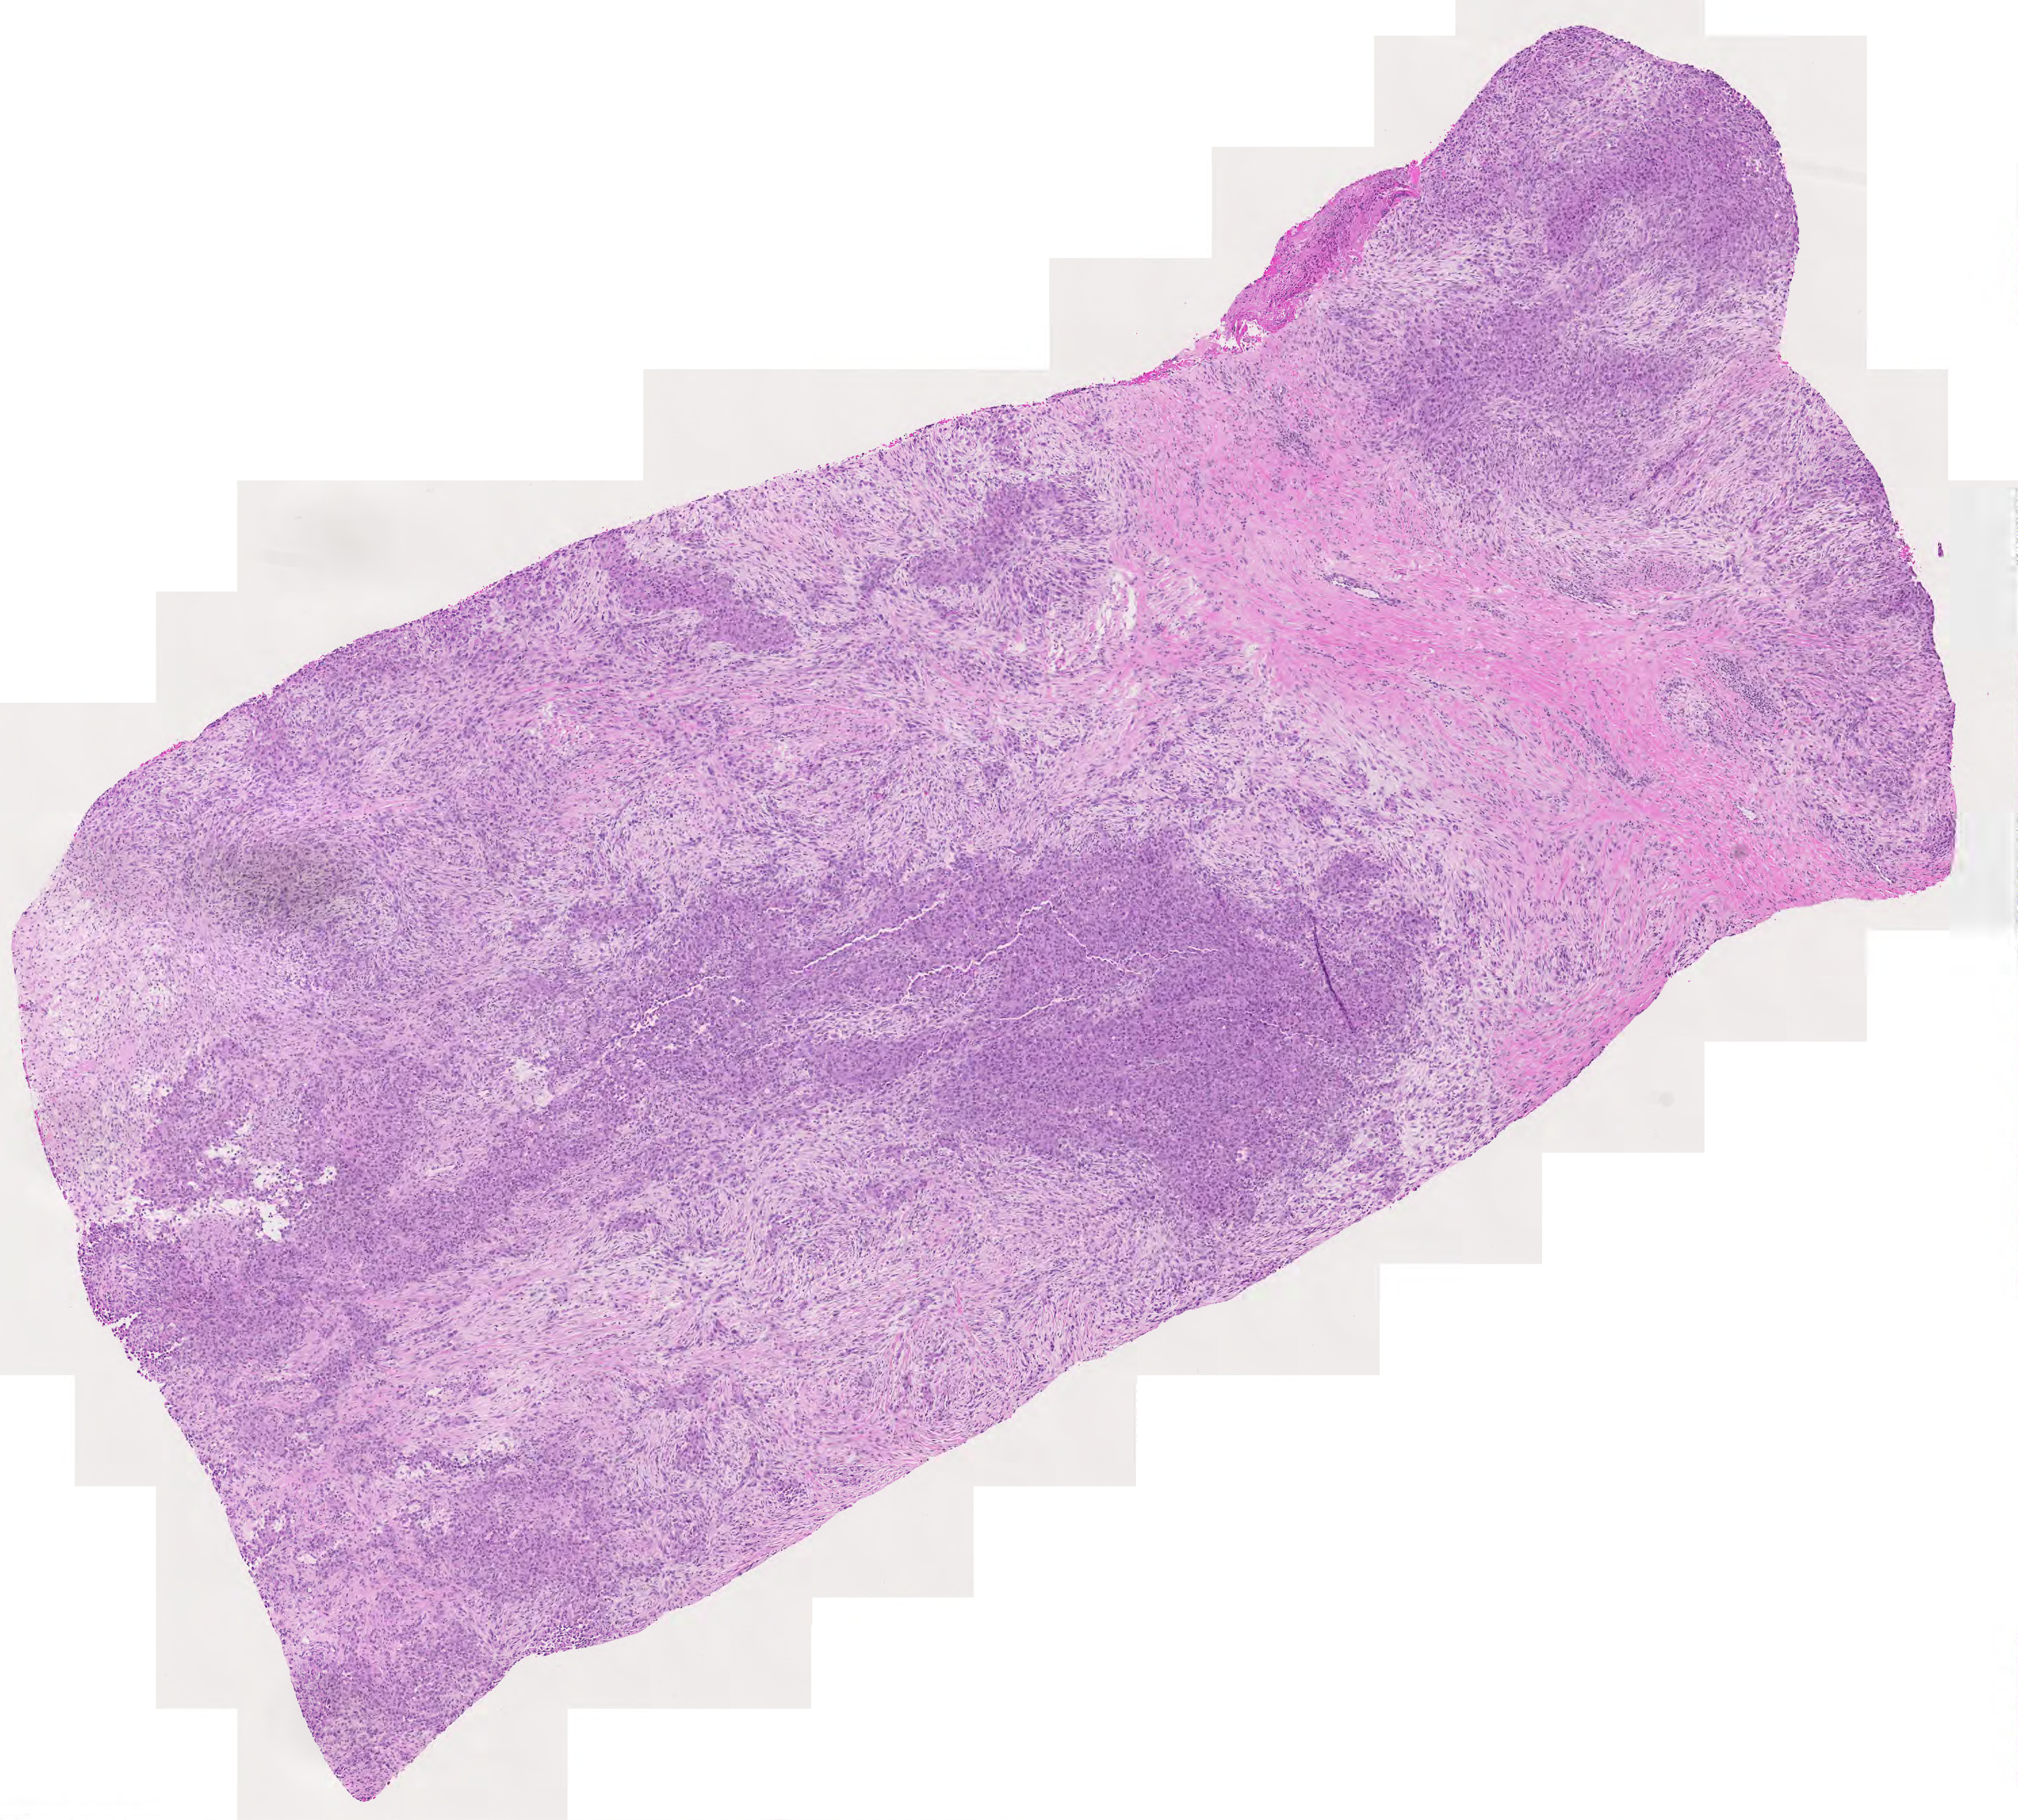
Digitized H&E-stained tissue section (whole slide), whole scanned area (about 7.7 x 6.9 mm, acquisition: 20x scan) shown as a low-resolution overview; tumour tissue sample. Patient: male, age 49 years.
- primary tumour site (as recorded): upper extremity
- patient diagnosis (cohort enrolment): sarcoma (site not recorded at cohort level)